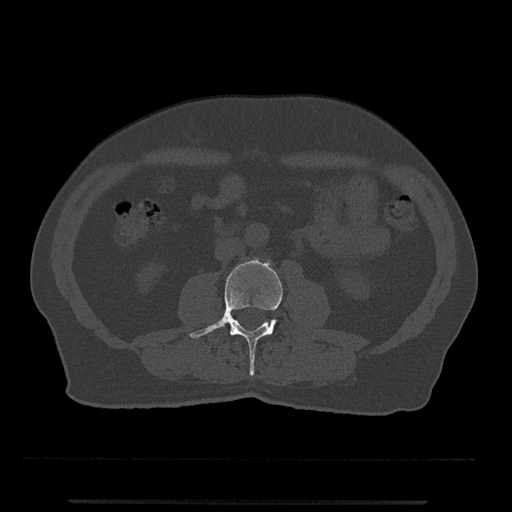
CT including the spine, one axial slice. Position 198 of 797 along the scan axis. Bone window (W 1800 / L 400 HU). 512 × 512 image matrix, field of view 419 × 419 mm. Patient: male, 63 years. From the clinical record (not read from this slice): primary cancer: prostate.
Structures marked on this image (semi-automatically segmented with operator editing):
- L3 vertebra: bounding box [x1, y1, x2, y2] px = [189, 258, 283, 376]